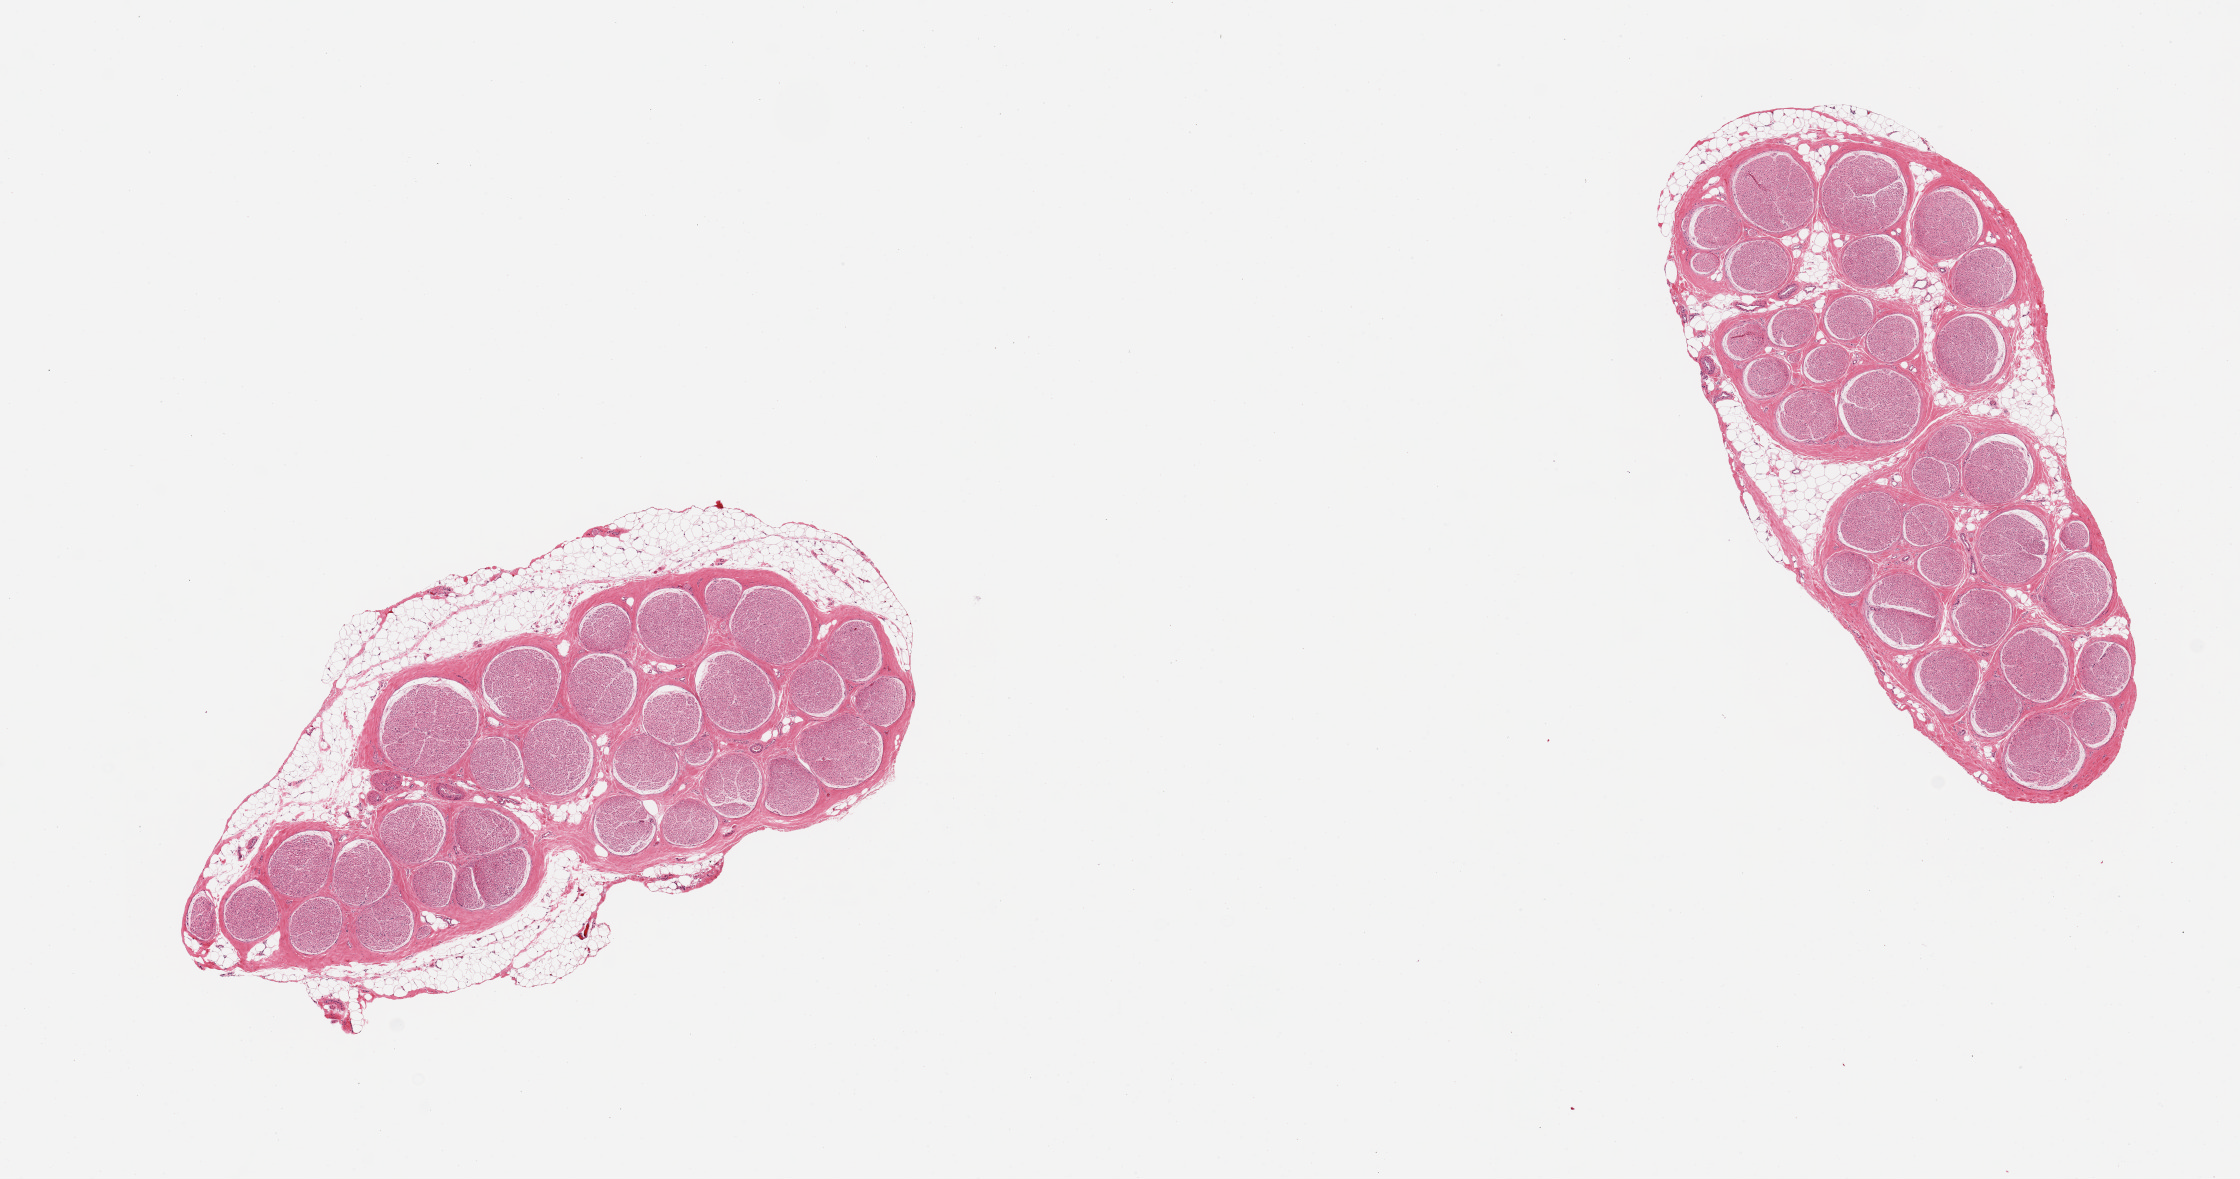
Hematoxylin and eosin (H&E) whole-slide image, brightfield — low-resolution overview of the scanned area, about 17.7 x 9.3 mm. PAXgene-fixed paraffin-embedded (PFPE) section. Target tissue: tibial nerve. Donor tissue sample.
Review note (as recorded): 2 pieces incomplete rim of adherent fat ~0.5-1mm.